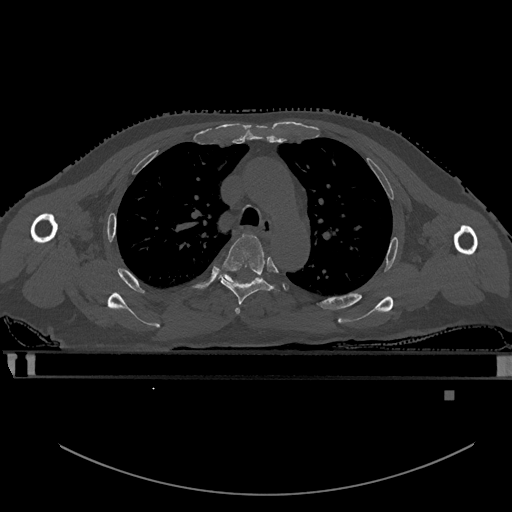
CT including the spine, one axial slice; position 402 of 969 along the scan axis; bone window (W 1800 / L 400 HU); 0.5 mm slice thickness; 512 × 512 image matrix, field of view 456 × 456 mm. Male patient, age 82 years. From the clinical record (not read from this slice): primary cancer: prostate; vertebrae with lytic lesions (as recorded): T11, T9, T8, T2.
Outlined on this slice (semi-automatically segmented with operator editing):
- T3 vertebra: box from (x=235, y=308) to (x=241, y=314) px
- T4 vertebra: (x=219, y=233)–(x=273, y=308)
- T5 vertebra: (x=216, y=271)–(x=255, y=284)